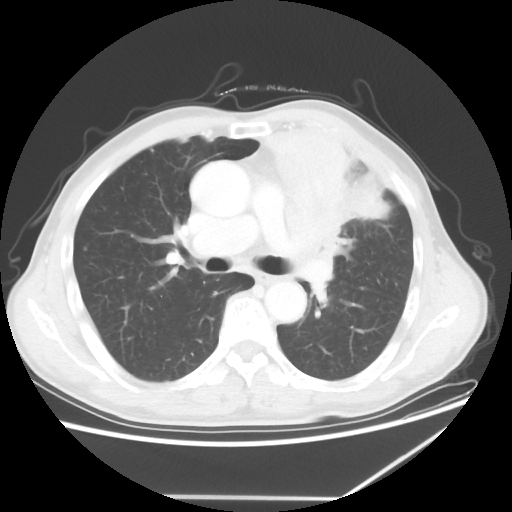
Chest CT, one axial slice; position 38 of 64 along the scan axis; reconstruction kernel STANDARD; lung window (W 1500 / L -600 HU); 5 mm slice thickness; 512 × 512 image matrix. Male patient, age 64 years. Case-level facts recorded for this patient, not image findings: clinical TNM (as recorded): T1c N1 M1.
Structures marked on this image (bounding box drawn by a radiologist):
- lung tumour (recorded histology: squamous cell carcinoma): bounding box (x1, y1, x2, y2) in pixels: (260, 115, 416, 308)